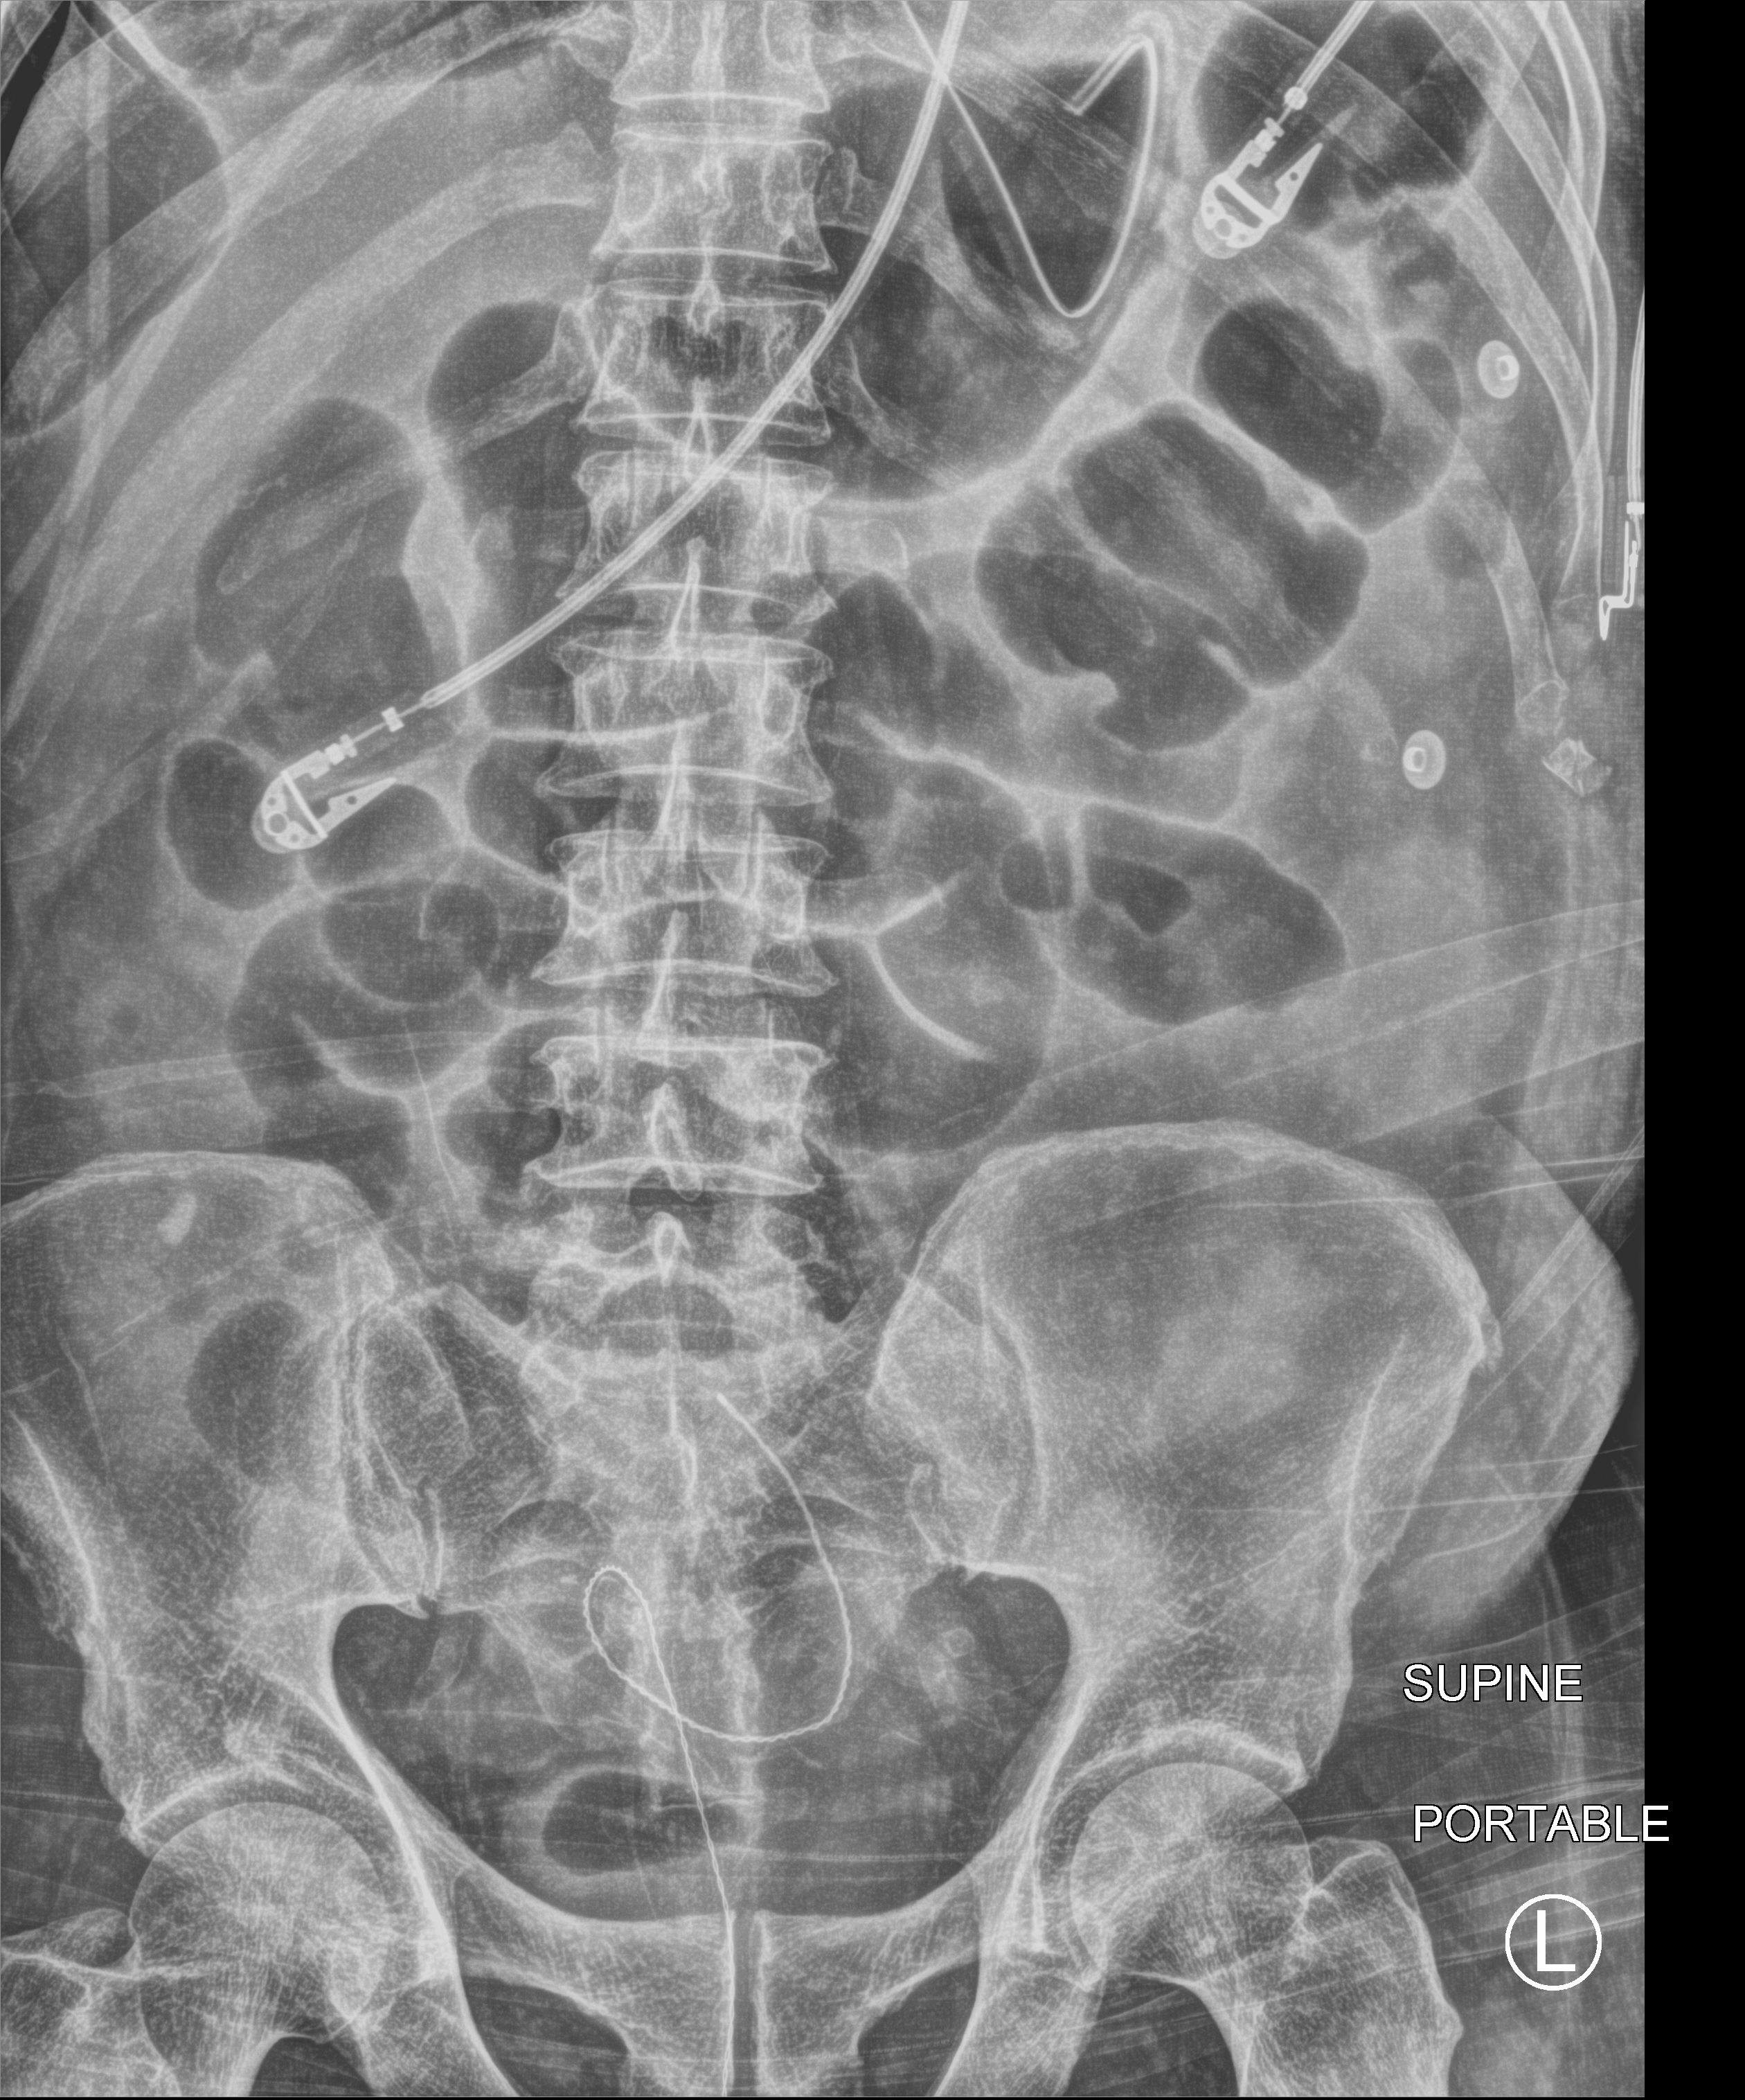
Bedside abdomen radiograph (computed radiography), anteroposterior (AP) projection. Male patient hospitalised with COVID-19, age 60–74 years.
From the hospital-stay record, not from the radiograph (when in the stay this image was taken is not recorded):
- hypertension (admission record): yes